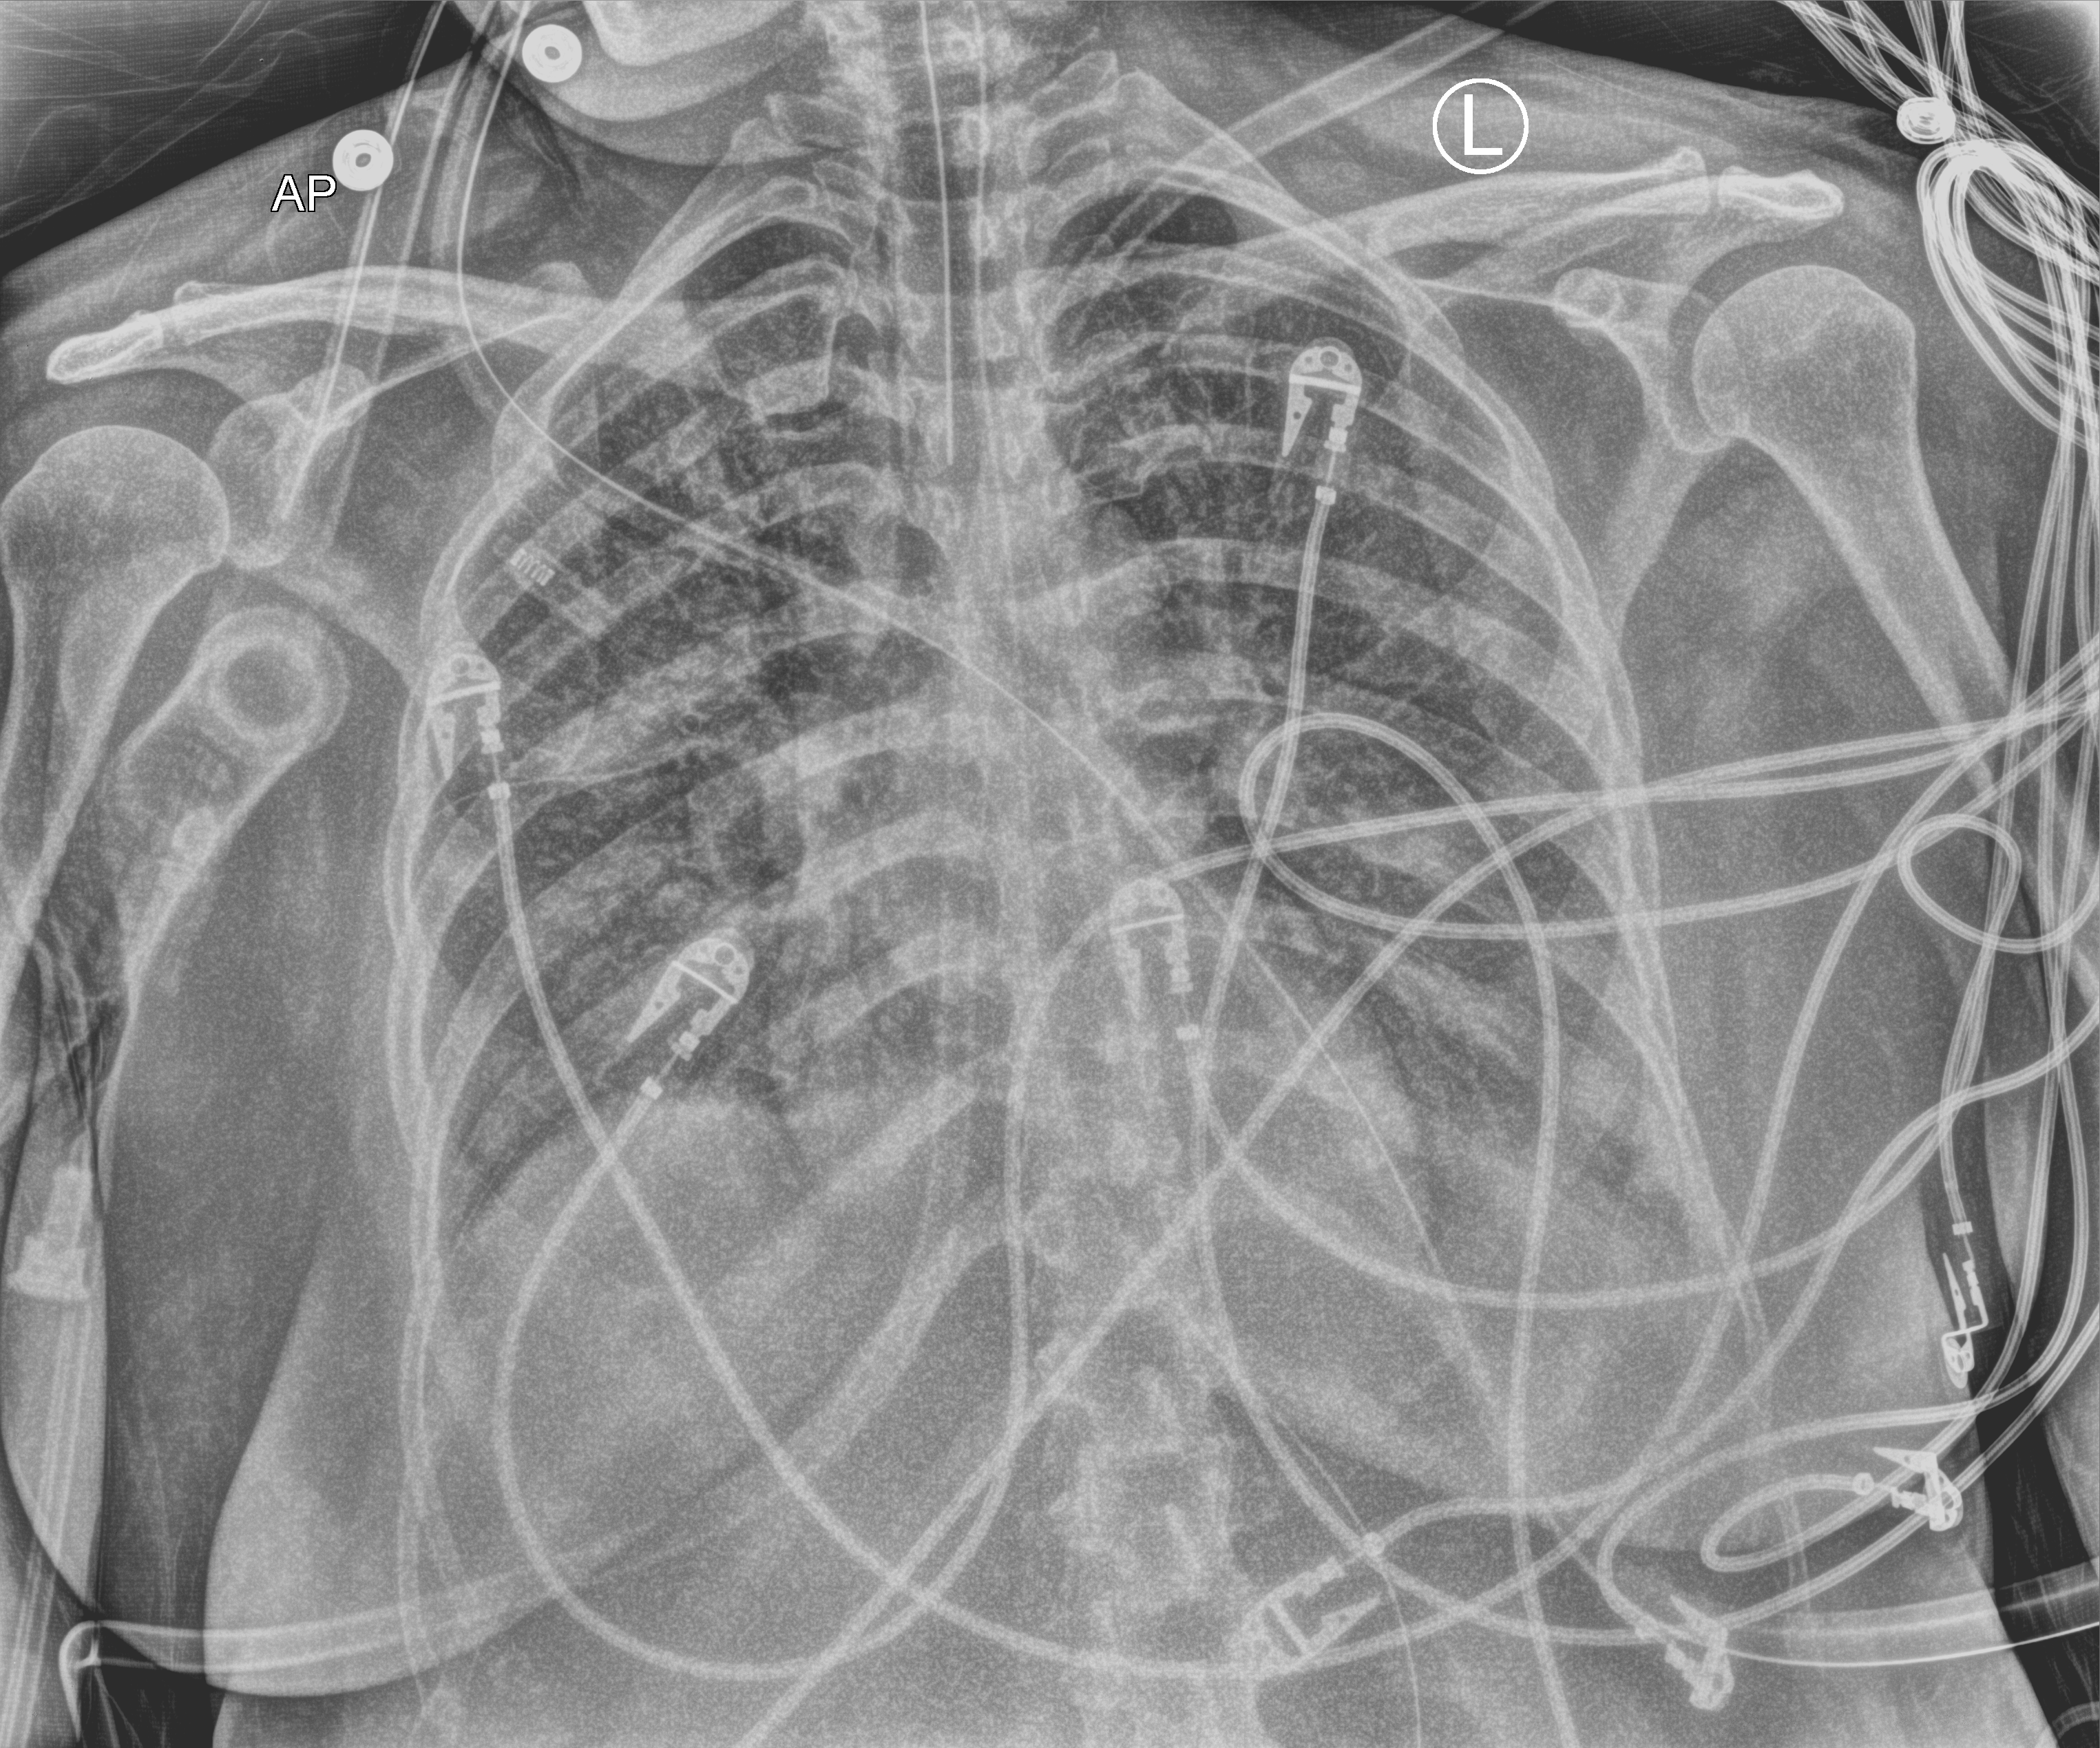
Portable chest radiograph, anteroposterior (AP) projection. Male patient hospitalised with COVID-19, age 18–59 years.
Admission-level facts for this patient (not findings on this image; timing relative to this image not recorded): admitted to intensive care during this hospital stay: yes.